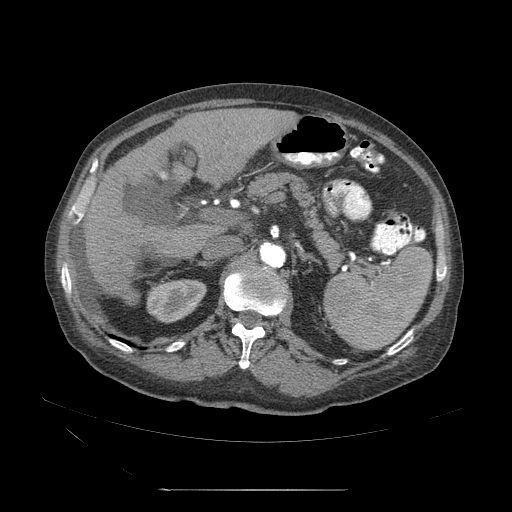
Contrast-enhanced abdominal CT (liver protocol), one axial slice. Slice 22 of 71 in the series (ordered by position). 120 kVp. Soft-tissue window (W 400 / L 40 HU). 2.5 mm slice thickness. 512 × 512 image matrix, field of view 440 × 440 mm. Case-level facts recorded for this patient, not image findings: diagnosis: hepatocellular carcinoma (patient treated with transarterial chemoembolisation; whether this scan precedes or follows treatment is not stated here); TNM stage (as recorded): Stage-II.
Outlined on this slice (semi-automatic segmentation, software-assisted and operator-edited):
- abdominal aorta: bounding box <261,244,286,270> (left, top, right, bottom; pixels)
- liver parenchyma outside the tumour (the mass and vessels are separate outlines, so this box may not span the whole liver): <83,112,278,300>
- liver vessels: <184,153,245,263>